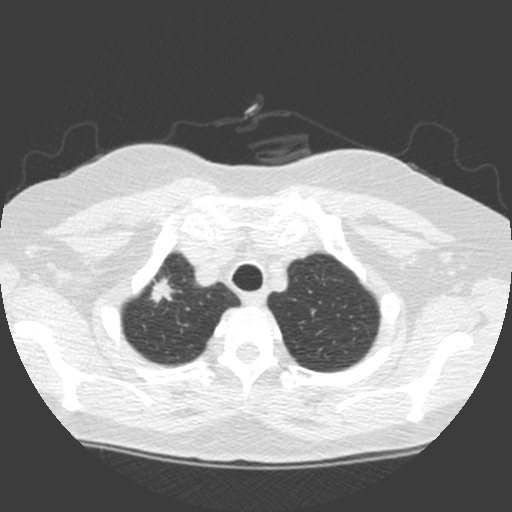
Chest CT (low-dose screening protocol), one axial image. First (baseline) screen. Lung window (W 1500 / L -600 HU). 2 mm slice thickness. Standard (soft-tissue) reconstruction kernel (C). 120 kVp. Slice 15 of 155 in the series. 512 × 512 image matrix, field of view 314 × 314 mm. Female participant, aged 63 years at enrolment.
Expert-annotated lung lesion, bounding box [x1, y1, x2, y2] px = [137, 271, 182, 309]. Reader record for this screening exam (exam-level; its link to the box is not recorded): non-calcified nodule or mass ≥4 mm, right upper lobe, 11 × 11 mm, spiculated (stellate) margins, soft tissue attenuation. Later outcome: lung cancer diagnosed 6 days after this screen — adenocarcinoma, NOS, right upper lobe, poorly differentiated (G3), stage IA (AJCC 6th edition), 17 mm at pathology.